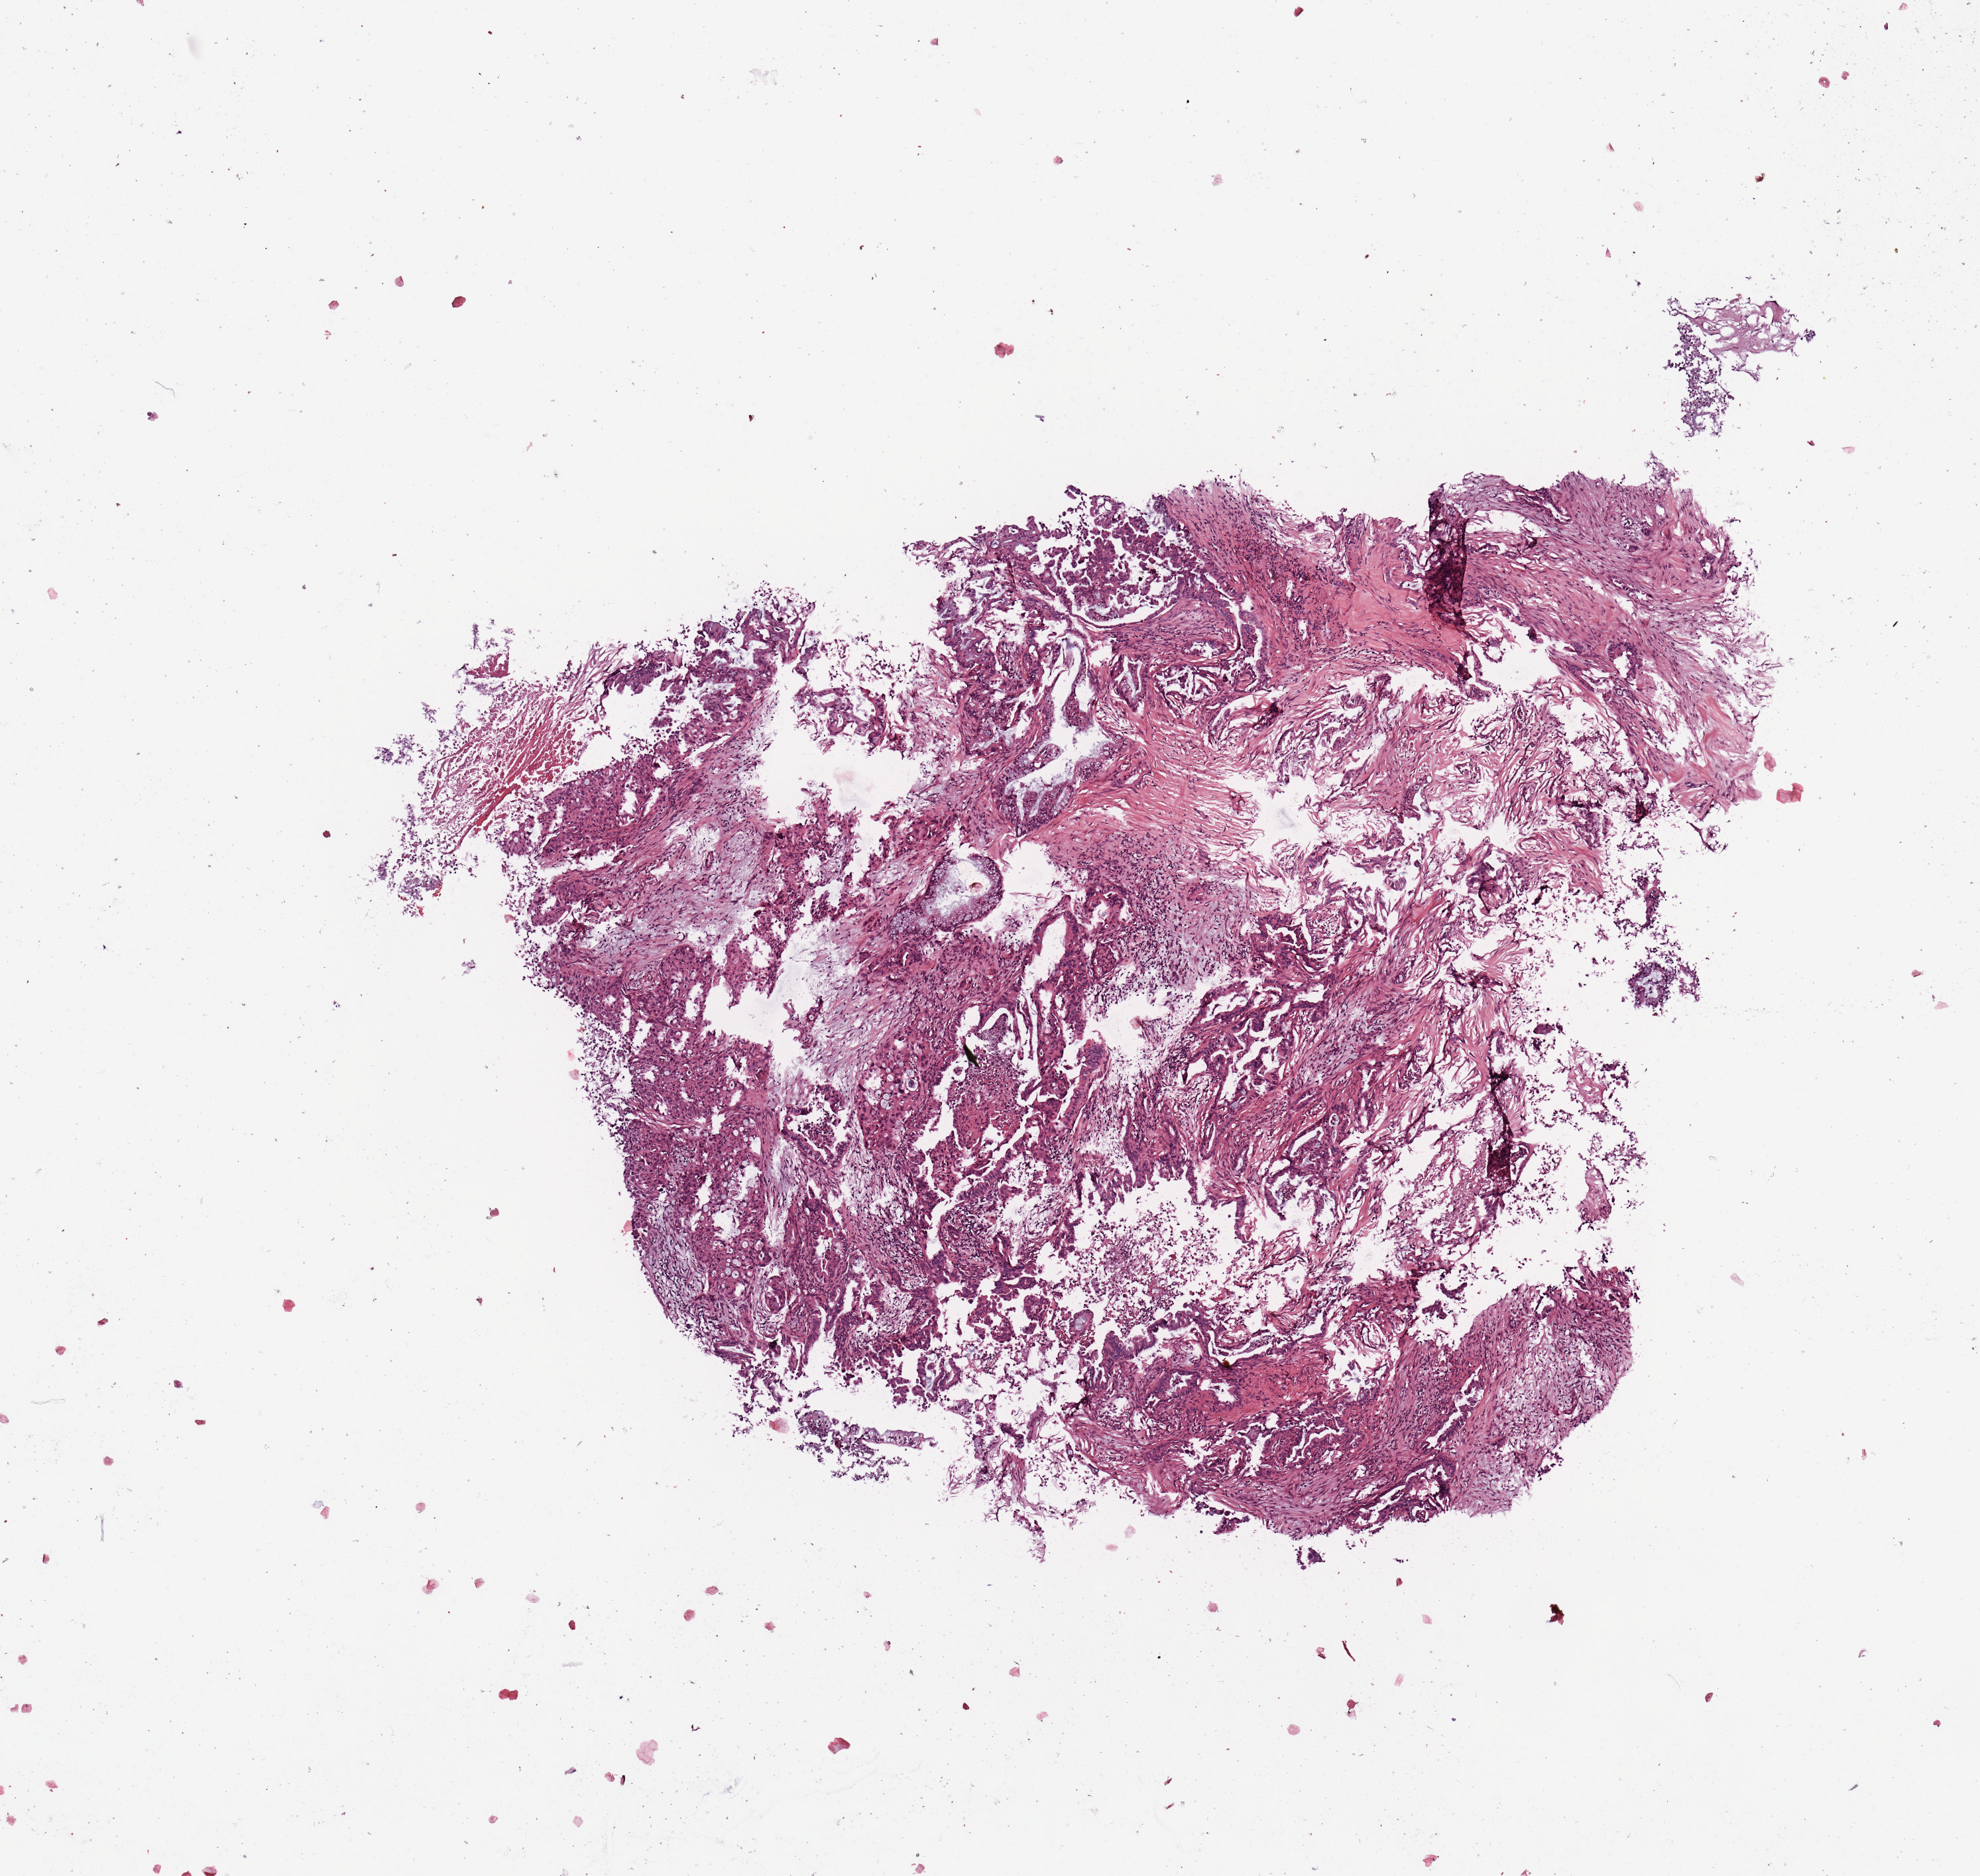
H&E whole-slide image, a low-resolution overview of the entire scanned area, about 5.9 x 5.6 mm; tumour tissue sample, sampled site: pancreas. Female, 63 y/o. Histologic grade: G2 (moderately differentiated). Pathologist review of this section (percent, as recorded): tumour nuclei 40%, necrosis 5%.
* AJCC pathologic stage: III
* diagnosis: Infiltrating duct carcinoma, NOS
* primary tumour site (as recorded): head